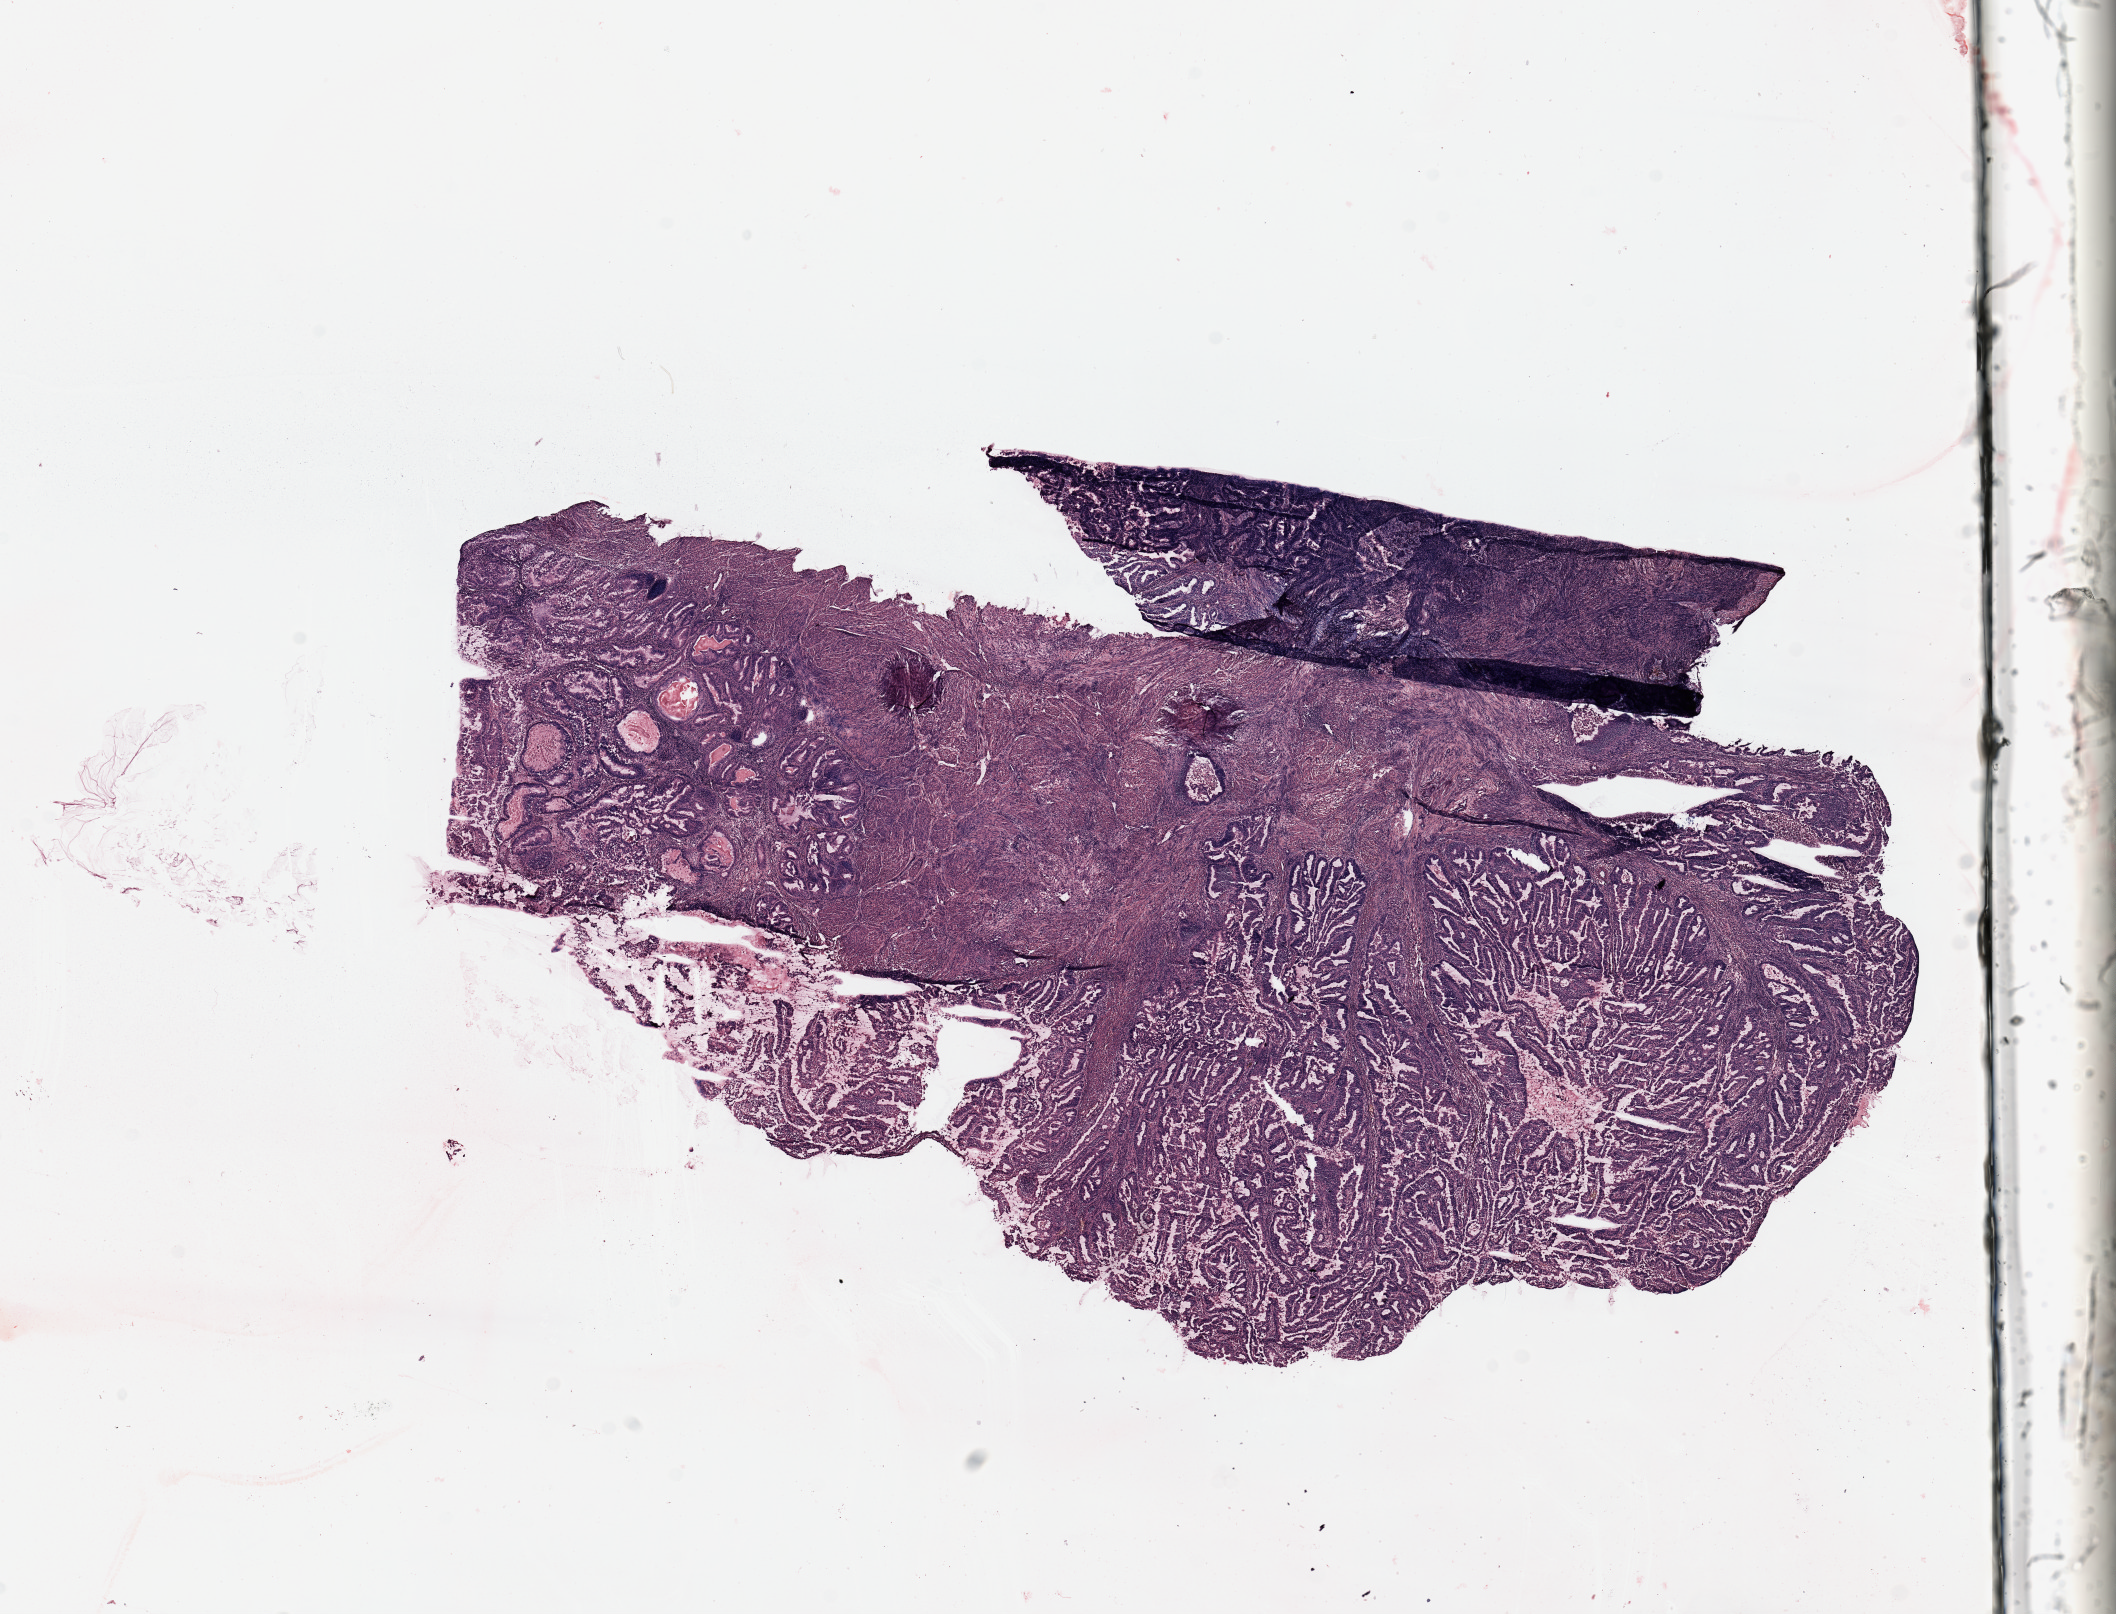
Digitized Hematoxylin and eosin (H&E) stained tissue section (whole slide) — whole scanned area (about 16.7 x 12.8 mm, slide scanned at 20x) shown as a low-resolution overview. Uterus, tumour tissue. Female, 66 y/o. Histologic grade: G2 (moderately differentiated).
• diagnosis: Endometrioid adenocarcinoma, NOS
• AJCC pathologic stage: II